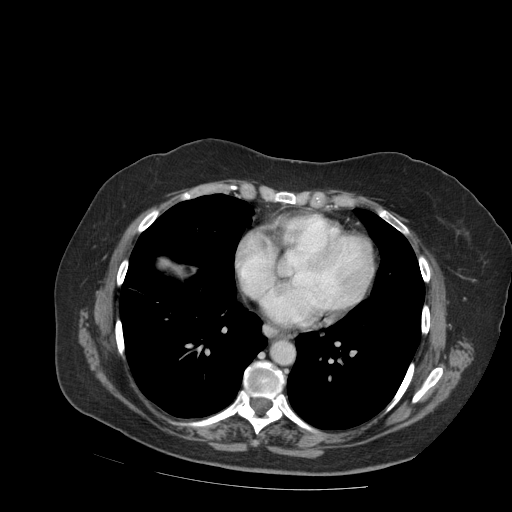
Contrast-enhanced abdominal CT (liver protocol), one axial slice. Slice 92 of 99 in the series (ordered by position). Reconstruction kernel STANDARD. 140 kVp. Soft-tissue window (W 400 / L 40 HU). 2.5 mm slice thickness. 512 × 512 image matrix. Case-level facts recorded for this patient, not image findings: diagnosis: hepatocellular carcinoma (patient treated with transarterial chemoembolisation; whether this scan precedes or follows treatment is not stated here); TNM stage (as recorded): Stage-IVB; Child-Pugh class: A.
Structures marked on this image (semi-automatic segmentation, software-assisted and operator-edited):
- liver parenchyma outside the tumour (the mass and vessels are separate outlines, so this box may not span the whole liver): bounding box [x1, y1, x2, y2] px = [160, 258, 196, 276]